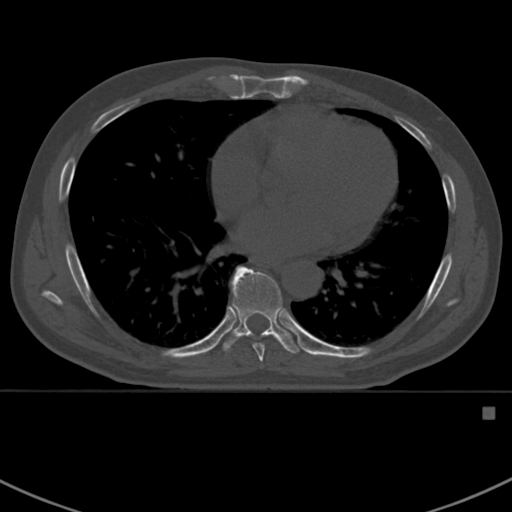
CT including the spine, one axial slice; slice 406 of 412 in the series (ordered by position); reconstruction kernel Br40s; bone window (W 1800 / L 400 HU); 1.5 mm slice thickness; 512 × 512 image matrix, field of view 358 × 358 mm. Patient: male, 59 years. From the clinical record (not read from this slice): primary cancer: prostate.
Outlined on this slice (semi-automatic segmentation, software-assisted and operator-edited):
- T7 vertebra: bounding box (x1, y1, x2, y2) in pixels: (253, 343, 265, 364)
- T8 vertebra: (222, 266, 302, 354)